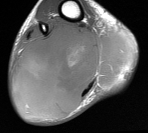
MRI of an extremity soft-tissue mass, one axial slice; position 32 of 76 along the scan axis; MR volume resampled by the dataset authors to the PET/CT grid (not the native acquisition matrix); 3.27 mm slice thickness; 148 × 133 image matrix. Male patient. From the clinical record (not read from this slice): histological type: liposarcoma - round cell; grade: high; site of the primary tumour: right calf.
Annotated regions visible in this slice (expert contour drawn on MRI and transferred to this co-registered scan by the dataset authors):
- gross tumour volume (mass): bounding box <11,21,135,116> (left, top, right, bottom; pixels)